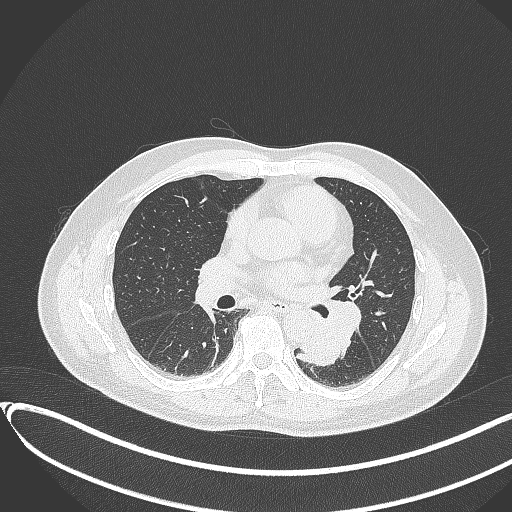
Chest CT, one axial slice; position 180 of 417 along the scan axis; lung window (W 1500 / L -600 HU); 1 mm slice thickness; 512 × 512 image matrix. Patient: male, 54 years. Case-level facts recorded for this patient, not image findings: clinical TNM (as recorded): T3 N0 M0.
Annotated regions visible in this slice (rectangle marked by the reading radiologist):
- lung tumour (recorded histology: squamous cell carcinoma): bounding box [x1, y1, x2, y2] px = [293, 316, 341, 370]